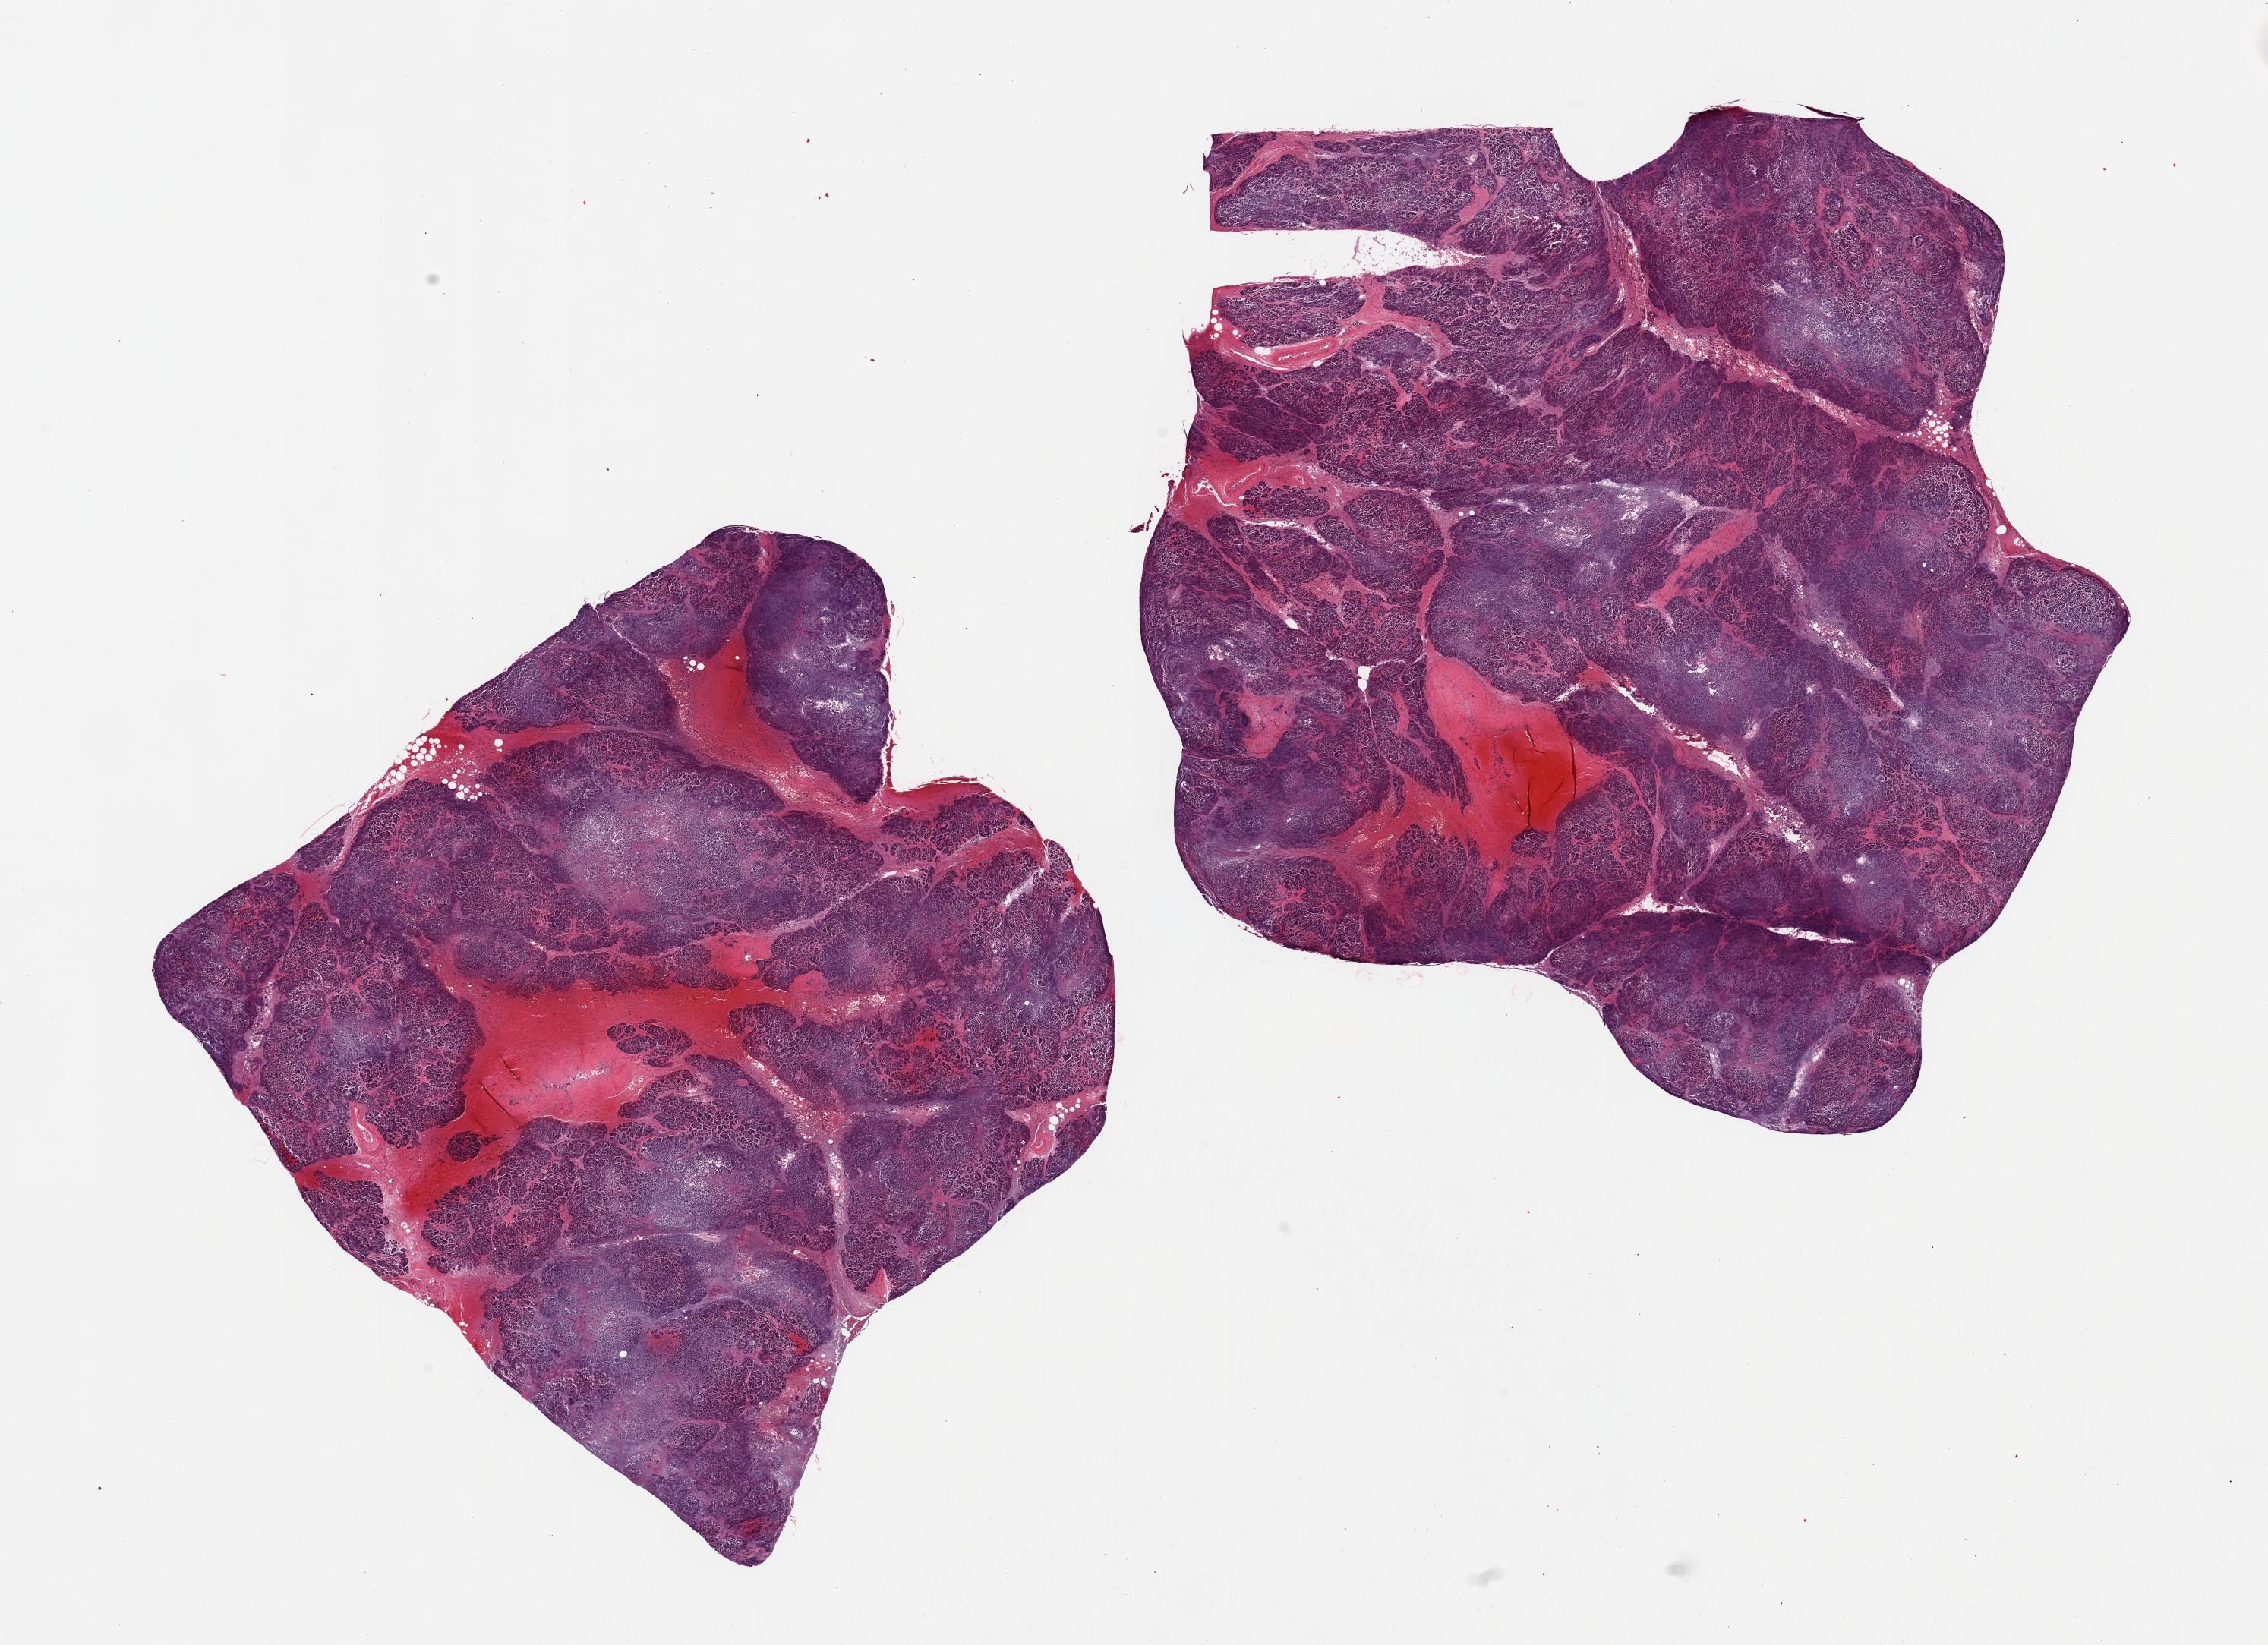
Digitized hematoxylin and eosin (H&E)-stained section, brightfield — shown as a low-resolution overview of the whole scanned area (about 23.6 x 17.1 mm); PAXgene-fixed, paraffin-embedded tissue; sampled site (target tissue): pancreas; tissue donor sample. Donor: male.
Reviewer comment on this tissue sample: 2 pieces. Advanced saponification/autolysis; Islets not well visualized.